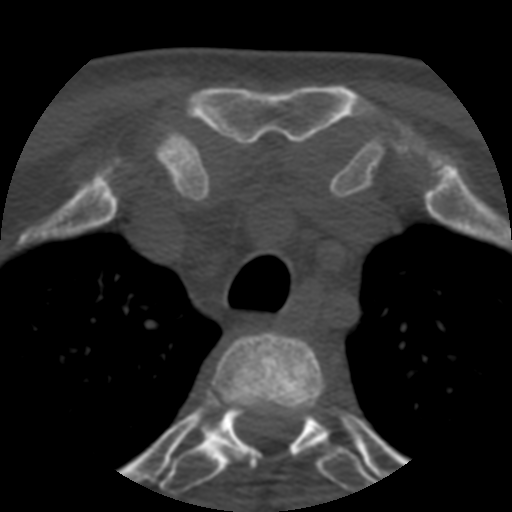
CT including the spine, one axial slice; position 422 of 508 along the scan axis; 120 kVp; bone window (W 1800 / L 400 HU); 512 × 512 image matrix, field of view 160 × 160 mm. Patient age 57 years. Case-level facts recorded for this patient, not image findings: primary cancer: prostate.
Outlined on this slice (semi-automatically segmented with operator editing):
- T2 vertebra: bounding box (x1, y1, x2, y2) in pixels: (213, 332, 327, 451)
- T3 vertebra: (160, 405, 376, 496)